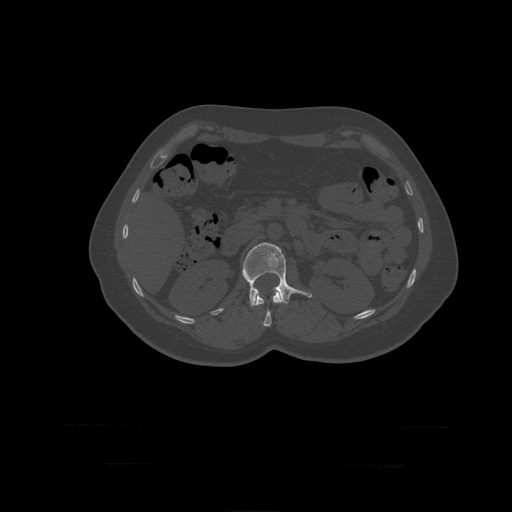
CT including the spine, one axial slice; position 158 of 399 along the scan axis; reconstruction kernel STANDARD; bone window (W 1800 / L 400 HU); 1.25 mm slice thickness; 512 × 512 image matrix, field of view 450 × 450 mm. Patient age 41 years. Case-level facts recorded for this patient, not image findings: primary cancer: breast.
Outlined on this slice (semi-automatically segmented with operator editing):
- L1 vertebra: bounding box [x1, y1, x2, y2] px = [255, 289, 283, 327]
- L2 vertebra: [242, 243, 312, 307]